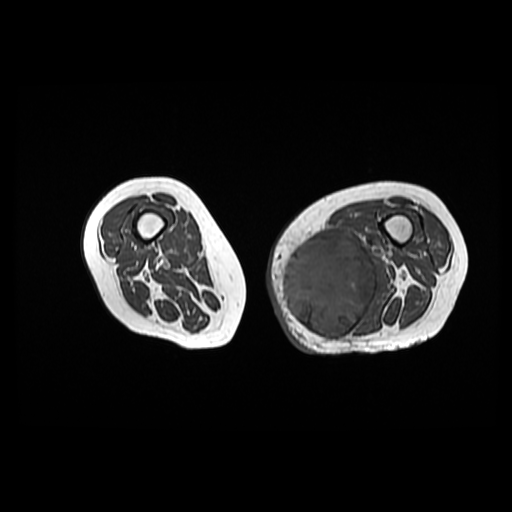
MRI of an extremity soft-tissue mass, one axial slice; slice 27 of 42 in the series (ordered by position); 512 × 512 image matrix, field of view 420 × 420 mm. Female patient. From the clinical record (not read from this slice): histological type: pleomorphic leiomyosarcoma; grade: high; site of the primary tumour: left thigh.
Outlined on this slice (outlined manually by an expert reader):
- gross tumour volume including surrounding oedema: bounding box (x1, y1, x2, y2) in pixels: (280, 234, 380, 338)
- gross tumour volume (mass): (280, 237, 378, 338)